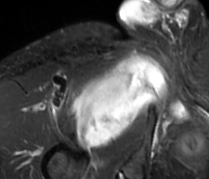
MRI of an extremity soft-tissue mass, one axial slice; slice 66 of 89 in the series (ordered by position); STIR; MR volume resampled by the dataset authors to the PET/CT grid (not the native acquisition matrix); 3.27 mm slice thickness; 209 × 179 image matrix, field of view 204 × 175 mm. Male patient. Case-level facts recorded for this patient, not image findings: histological type: undifferentiated - pleiomorphic; grade: high; site of the primary tumour: right thigh.
Outlined on this slice (expert contour drawn on MRI and transferred to this co-registered scan by the dataset authors):
- gross tumour volume including surrounding oedema: bounding box [x1, y1, x2, y2] px = [71, 53, 166, 147]
- gross tumour volume (mass): [71, 55, 165, 149]